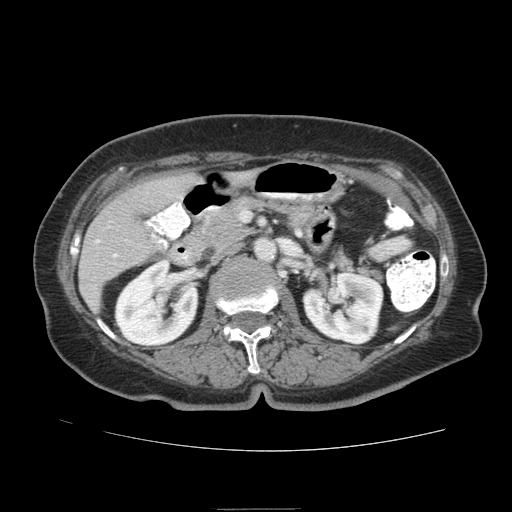
Contrast-enhanced abdominal CT (liver protocol), one axial slice. Position 33 of 95 along the scan axis. Soft-tissue window (W 400 / L 40 HU). 2.5 mm slice thickness. 512 × 512 image matrix, field of view 360 × 360 mm. Case-level facts recorded for this patient, not image findings: diagnosis: hepatocellular carcinoma (patient treated with transarterial chemoembolisation; whether this scan precedes or follows treatment is not stated here); TNM stage (as recorded): Stage-IVA; Child-Pugh class: B; tumour differentiation: moderately differentiated; tumour nodularity: uninodular.
Structures marked on this image (semi-automatically segmented with operator editing):
- liver parenchyma outside the tumour (the mass and vessels are separate outlines, so this box may not span the whole liver): bounding box <78,170,258,310> (left, top, right, bottom; pixels)
- liver vessels: <96,234,160,257>